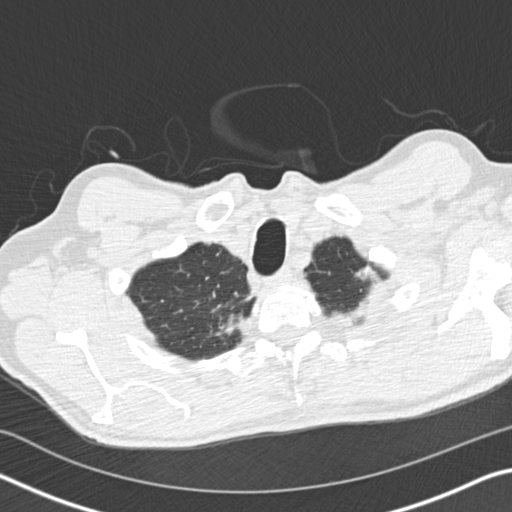
Low-dose screening chest CT, one axial slice; slice 158 of 175 in the series (ordered by position); lung window (W 1500 / L -600 HU); 2 mm slice thickness; 512 × 512 image matrix, field of view 340 × 340 mm.
Annotated regions visible in this slice (outlined manually by an expert reader):
- lesion 1 (tumor, upper lobe of right lung): box from (x=220, y=310) to (x=246, y=334) px